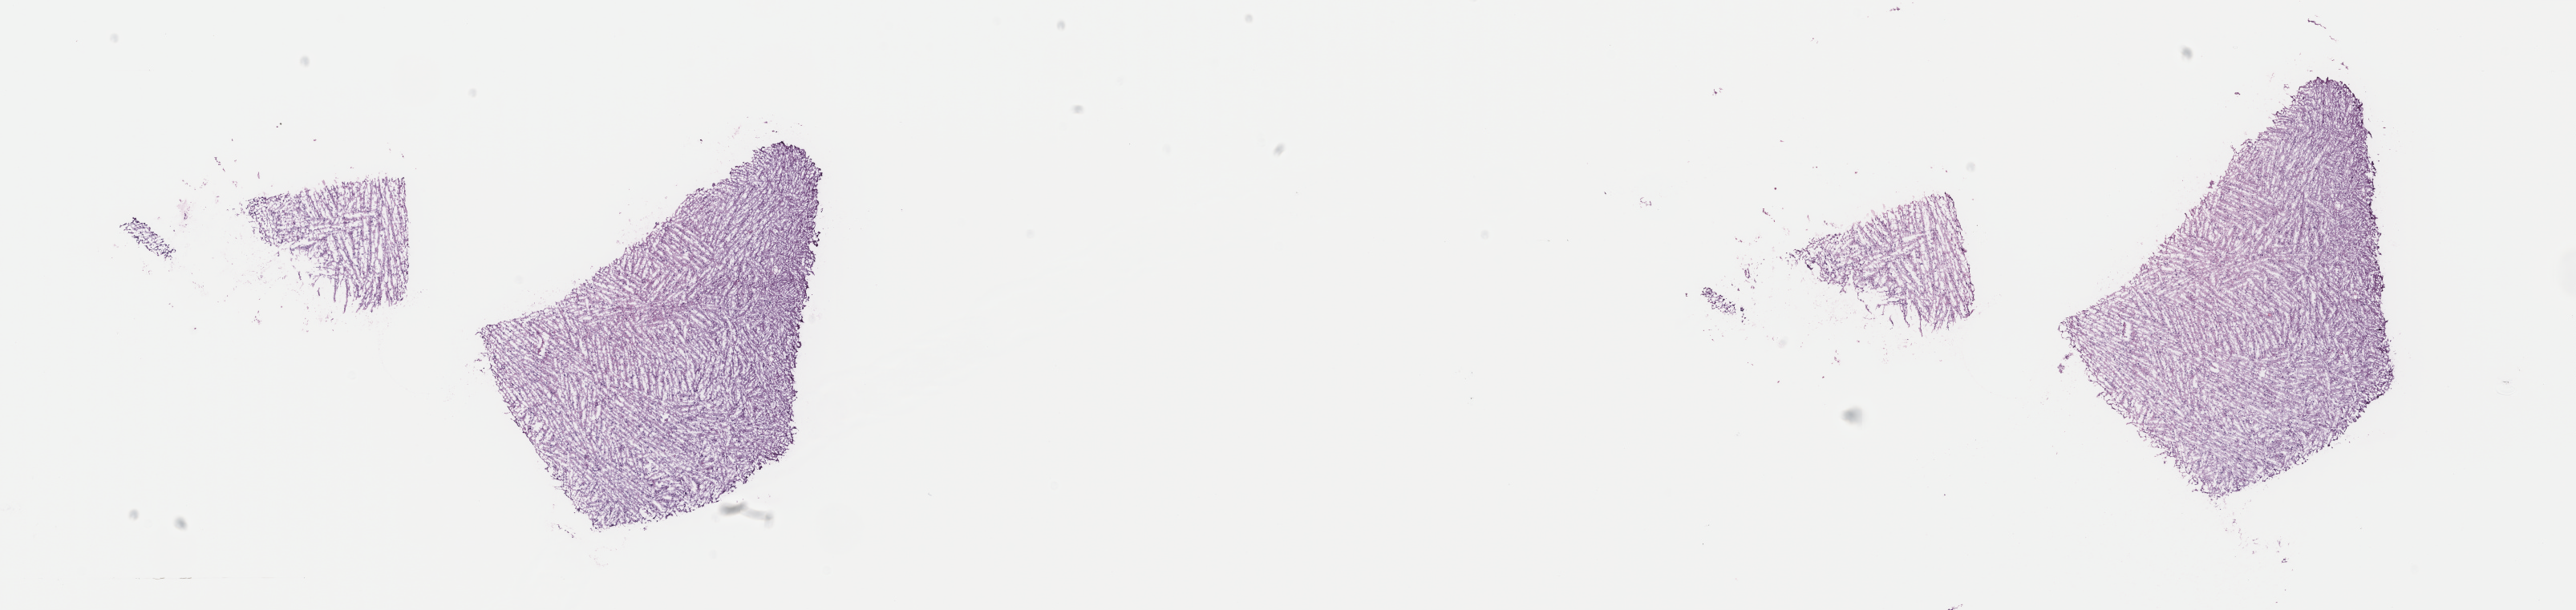
Digitized H&E tissue section (whole slide) — whole scanned area (about 25.5 x 6.0 mm, from a 40x scan) shown as a low-resolution overview; frozen section from the top of the tissue portion; brain, primary tumour sample. Male, age 27 years at initial diagnosis. Histologic grade: G2 (moderately differentiated). Slide review estimates, as recorded: tumour cells 40%, tumour nuclei 80%, normal cells 10%, stromal cells 50%, necrosis 0%. Inflammatory infiltration, as recorded: lymphocyte infiltration 0%, monocyte infiltration 0%, neutrophil infiltration 0%.
* pathologic diagnosis: Mixed glioma (cerebrum)